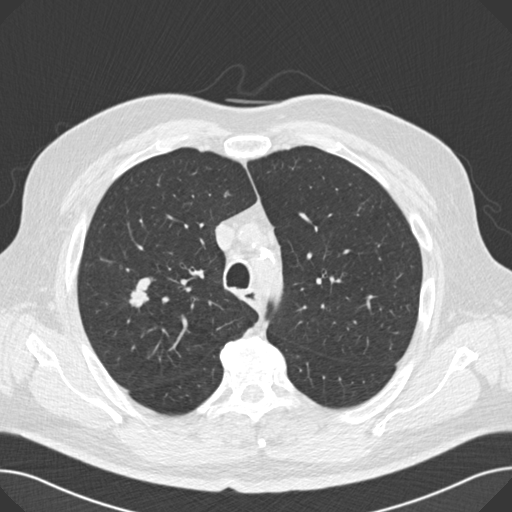
Chest CT (low-dose screening protocol), one axial image. Second screening round (one year after baseline). Lung window (W 1500 / L -600 HU). Slice 46 of 166 in the series. 512 × 512 image matrix, field of view 374 × 374 mm. Male, age 67 years at enrolment. Current smoker at enrolment.
Lesion marked by an expert reader, box from (x=121, y=274) to (x=162, y=312) px. Screening reader's record for this exam: no non-calcified nodule ≥4 mm recorded. Official screen result: negative screen, significant abnormalities not suspicious for lung cancer. Later outcome: lung cancer diagnosed 194 days after this screen — small cell carcinoma, NOS, right middle lobe, stage IA (AJCC 6th edition), 20 mm at pathology.